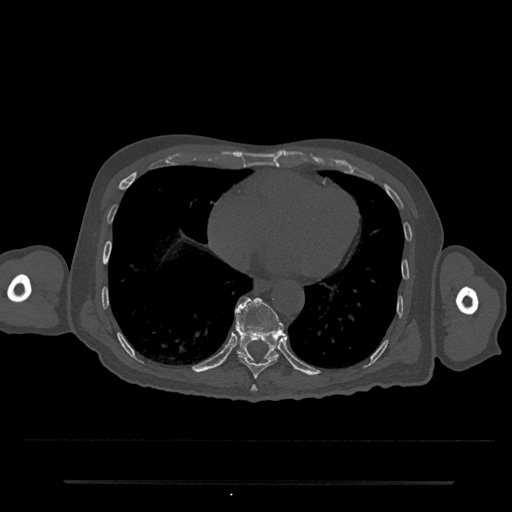
CT including the spine, one axial slice; slice 343 of 797 in the series (ordered by position); 120 kVp; bone window (W 1800 / L 400 HU); 0.5 mm slice thickness; 512 × 512 image matrix, field of view 427 × 427 mm. Male patient, age 74 years. From the clinical record (not read from this slice): primary cancer: prostate.
Structures marked on this image (semi-automatic segmentation, software-assisted and operator-edited):
- T10 vertebra: bounding box <235,296,285,361> (left, top, right, bottom; pixels)
- T8 vertebra: <251,385,258,392>
- T9 vertebra: <237,354,279,379>